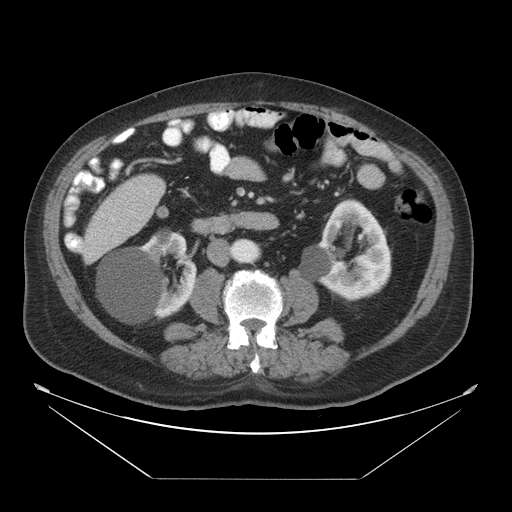
Contrast-enhanced abdominal CT, one axial slice; slice 12 of 45 in the series (ordered by position); soft-tissue window (W 400 / L 40 HU); 5 mm slice thickness; 512 × 512 image matrix. Male patient, age 87 years. Case-level facts recorded for this patient, not image findings: diagnosis: colorectal cancer liver metastases, imaged before liver resection; multiple liver metastases: no; largest metastasis: 4.5 cm; disease in both lobes: yes.
Annotated regions visible in this slice (manually delineated by an expert):
- liver: bounding box (x1, y1, x2, y2) in pixels: (82, 173, 166, 264)